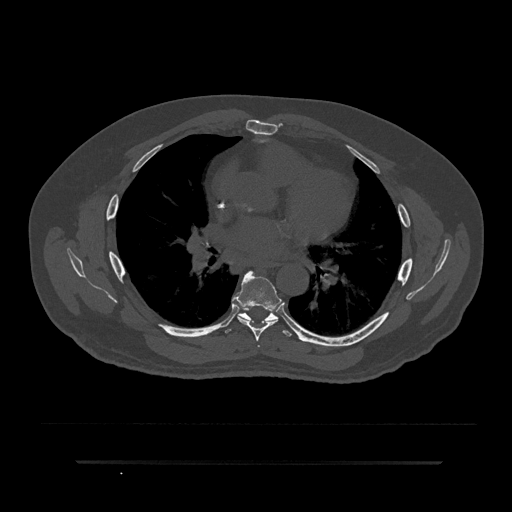
CT including the spine, one axial slice. Position 509 of 797 along the scan axis. Reconstruction kernel Br40s/3. Bone window (W 1800 / L 400 HU). 512 × 512 image matrix, field of view 464 × 464 mm. Male patient, age 59 years. Case-level facts recorded for this patient, not image findings: primary cancer: bile ducts.
Annotated regions visible in this slice (semi-automatically segmented with operator editing):
- T5 vertebra: bounding box [x1, y1, x2, y2] px = [258, 345, 260, 347]
- T6 vertebra: [233, 271, 282, 341]
- T7 vertebra: [225, 306, 294, 337]